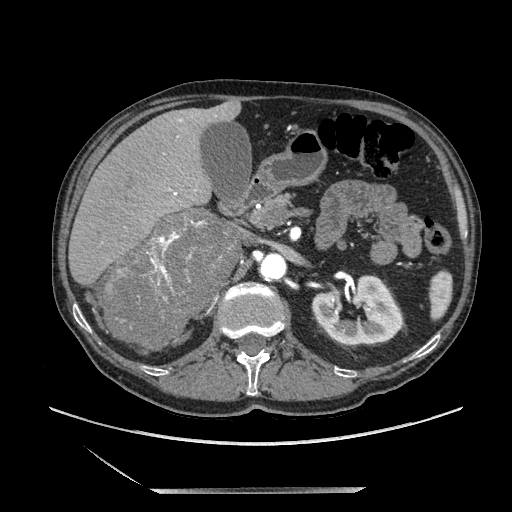
Contrast-enhanced abdominal CT, one axial slice; position 115 of 243 along the scan axis; soft-tissue window (W 400 / L 40 HU); 512 × 512 image matrix. Male patient. From the clinical record (not read from this slice): diagnosis: adrenocortical carcinoma; tumour side: right adrenal; tumour size at pathology: 16 cm; Ki-67 index: 17 %; stage (as recorded): 3.
Outlined on this slice (semi-automatic segmentation, software-assisted and operator-edited):
- mass: bounding box <104,210,239,345> (left, top, right, bottom; pixels)